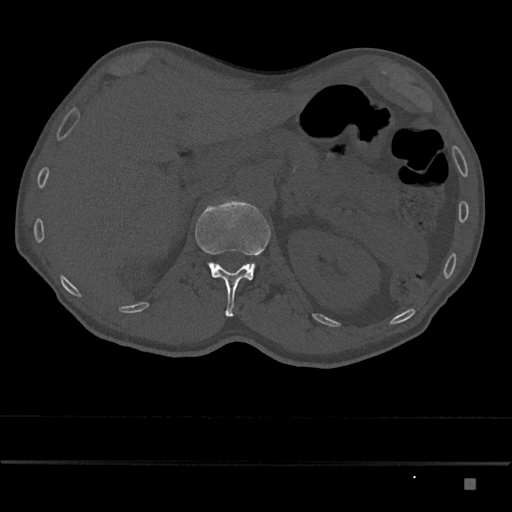
CT including the spine, one axial slice. Bone window (W 1800 / L 400 HU). 0.5 mm slice thickness. 512 × 512 image matrix, field of view 390 × 390 mm. Patient: male, 72 years. From the clinical record (not read from this slice): primary cancer: prostate.
Structures marked on this image (semi-automatic segmentation, software-assisted and operator-edited):
- L1 vertebra: box from (x=195, y=199) to (x=271, y=317) px